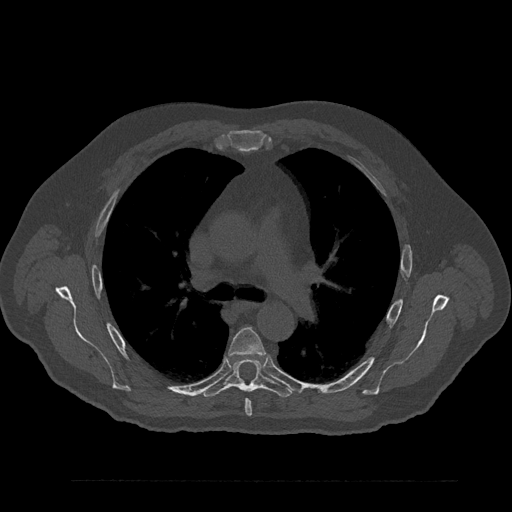
CT including the spine, one axial slice; bone window (W 1800 / L 400 HU); 512 × 512 image matrix. Male patient, age 61 years. From the clinical record (not read from this slice): primary cancer: prostate.
Structures marked on this image (semi-automatically segmented with operator editing):
- T5 vertebra: box from (x=228, y=328) to (x=265, y=416) px
- T6 vertebra: (x=201, y=357)–(x=293, y=397)